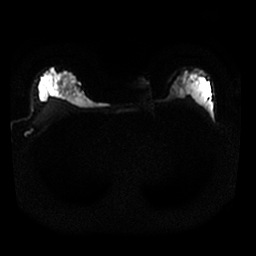
Breast MRI, one axial slice; diffusion-weighted series; image 2 of 4 stored at this slice position (different b-values; order by instance number); 1.5 T; 4 mm slice thickness; 256 × 256 image matrix, field of view 320 × 320 mm. Female patient.
Annotated regions visible in this slice (manually delineated by an expert):
- tumour on diffusion-weighted imaging: bounding box (x1, y1, x2, y2) in pixels: (171, 85, 184, 100)